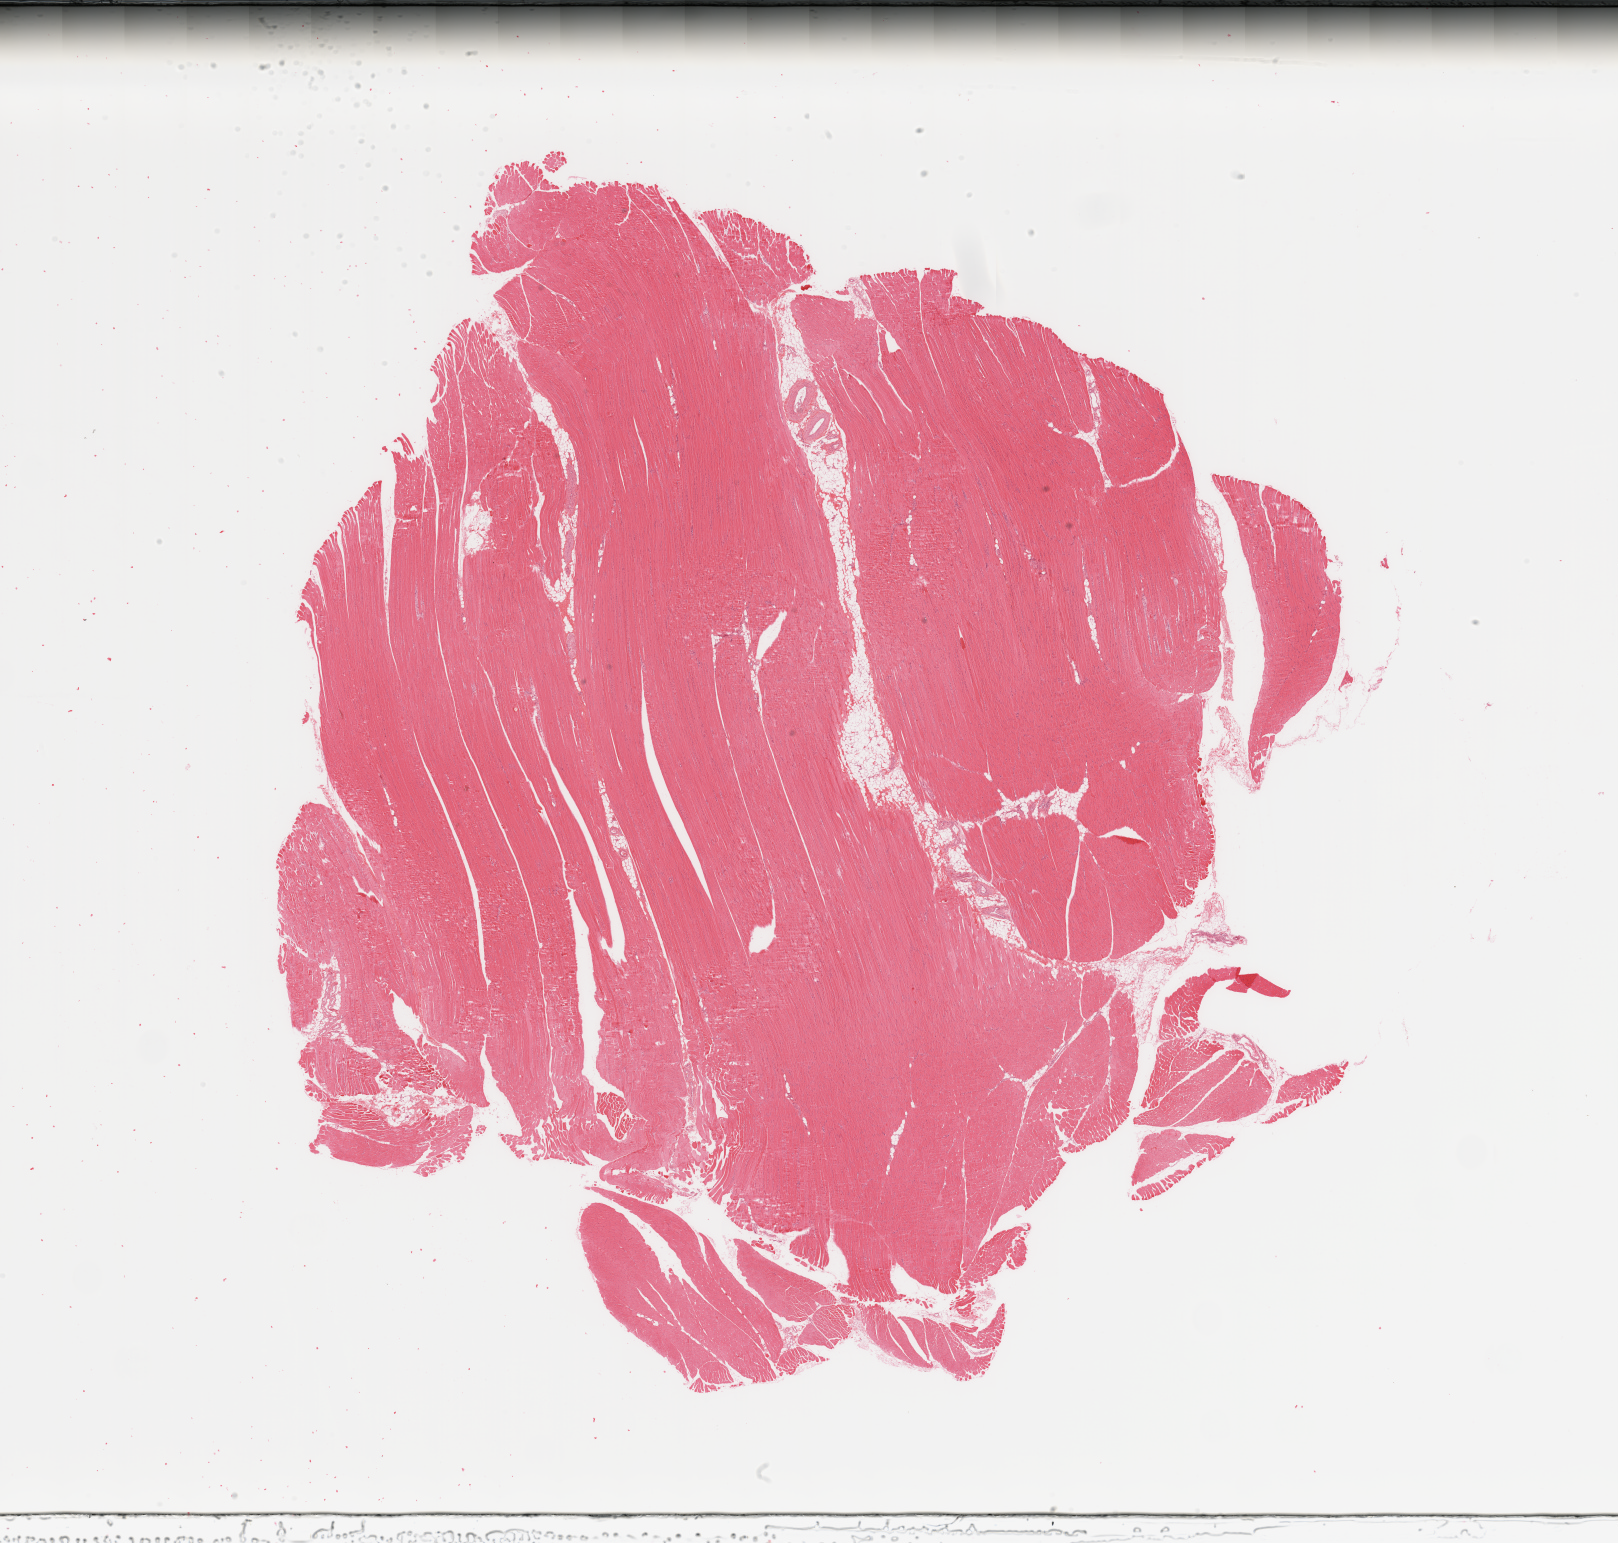
H&E-stained whole-slide image — whole scanned area (about 25.6 x 24.4 mm) shown as a low-resolution overview; normal (non-tumour) tissue sample. Patient: female, age 32 years.
• this section: normal (non-tumour) tissue from the same patient
• patient diagnosis (cohort enrolment): sarcoma (site not recorded at cohort level)